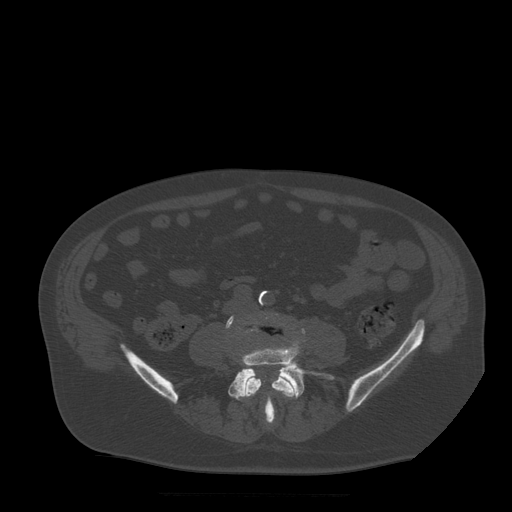
CT including the spine, one axial slice. Slice 100 of 522 in the series (ordered by position). Bone window (W 1800 / L 400 HU). 512 × 512 image matrix, field of view 420 × 420 mm. Patient age 72 years. Case-level facts recorded for this patient, not image findings: primary cancer: prostate.
Annotated regions visible in this slice (semi-automatic segmentation, software-assisted and operator-edited):
- L4 vertebra: bounding box <233,317,298,398> (left, top, right, bottom; pixels)
- L5 vertebra: <226,316,334,422>